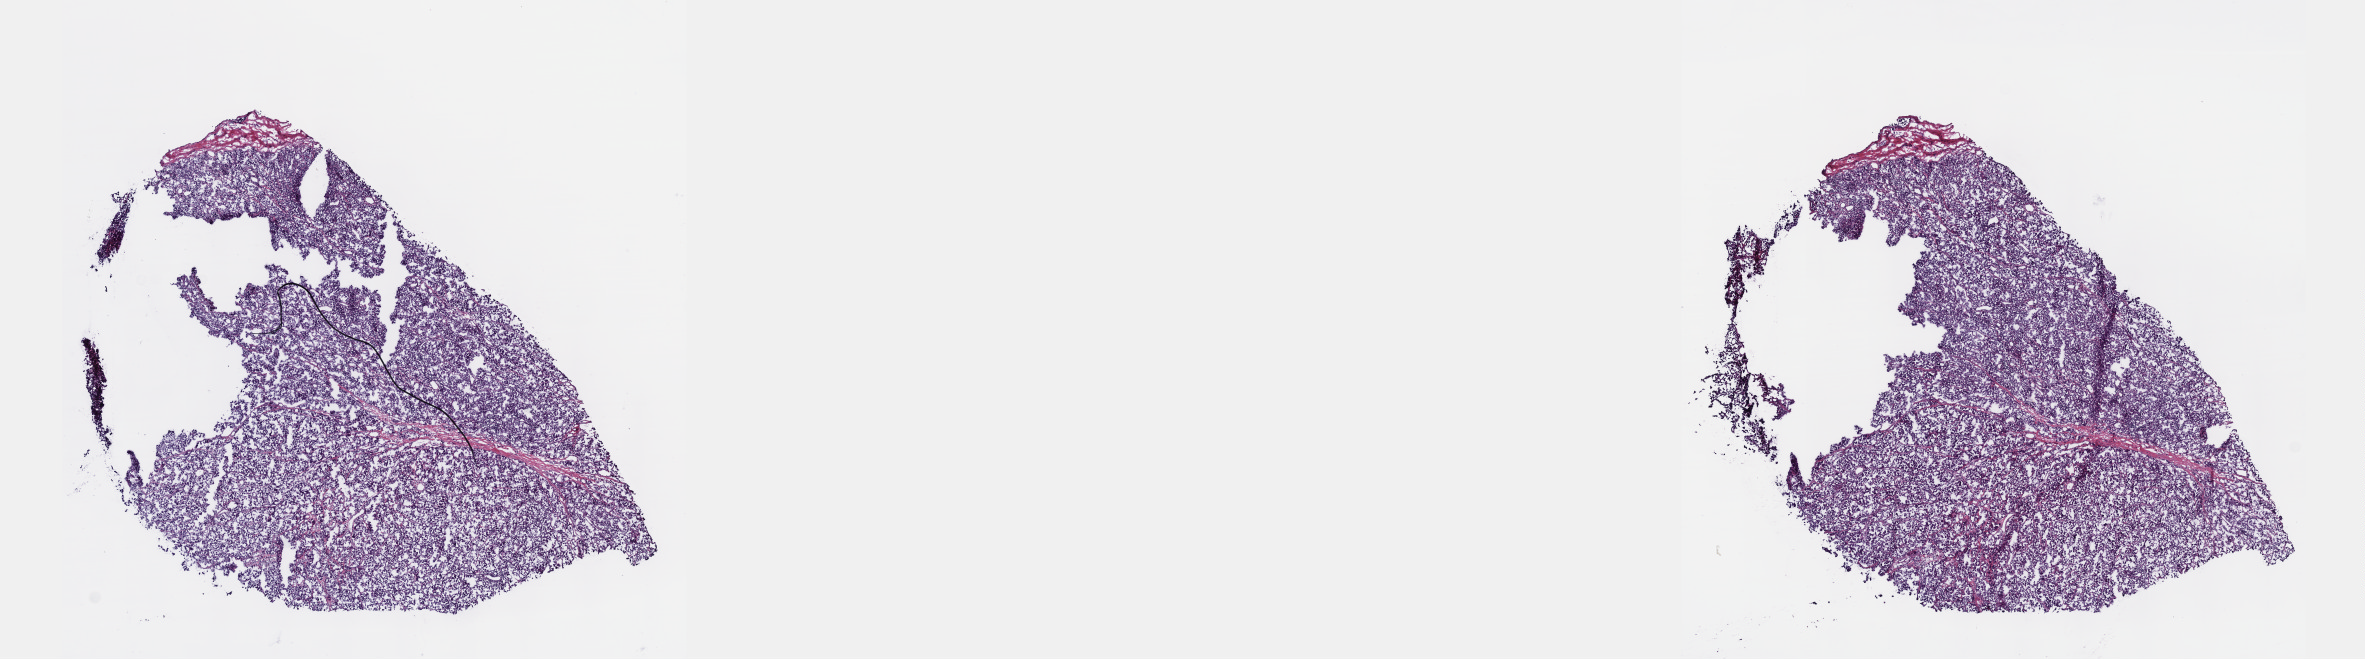
Digitized Hematoxylin and eosin (H&E) stained tissue section (whole slide), shown as a low-resolution overview of the whole scanned area (about 19.1 x 5.3 mm, from a 40x scan), frozen section from the top of the tissue portion, metastatic tumour sample, sampled site not recorded. Patient: male, age at initial diagnosis 57 years. Composition of this section per pathologist review: tumour cells 100%, tumour nuclei 95%, normal cells 0%, stromal cells 0%, necrosis 0%. Inflammatory infiltration, as recorded: lymphocyte infiltration 0%, monocyte infiltration 0%, neutrophil infiltration 0%.
* this section: metastatic tumour tissue
* patient diagnosis: Malignant melanoma, NOS